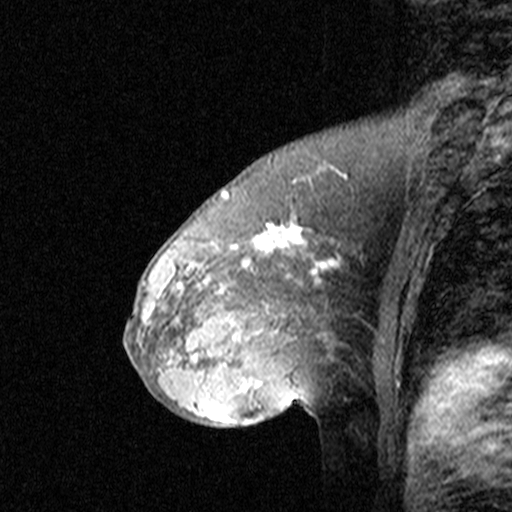
Breast MRI (dynamic contrast-enhanced), one sagittal slice; dynamic contrast-enhanced study with each time point stored as its own series, time point 2 of 3 at this slice position (early post-contrast, ordered by acquisition time); 1.5 T; TE 4.5 ms, TR 11 ms; 512 × 512 image matrix. Patient: female, 46 years. Case-level facts recorded for this patient, not image findings: setting: breast cancer imaged before/during neoadjuvant chemotherapy; receptor status: HER2-positive.
Annotated regions visible in this slice (semi-automatically segmented with operator editing):
- analysis volume of interest (the breast-tissue region the enhancement analysis was run in; not a lesion): box from (x=144, y=172) to (x=359, y=393) px
- tumour enhancement mask (voxels above the 90 % enhancement threshold inside the analysis volume of interest): (x=144, y=175)–(x=347, y=393)